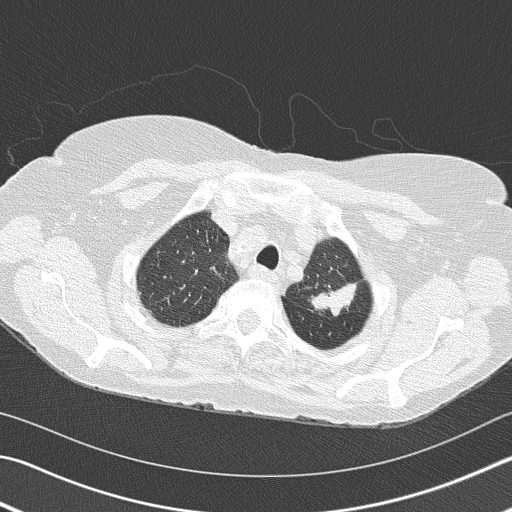
Chest CT (low-dose screening protocol), one axial image; second screening round (one year after baseline); lung window (W 1500 / L -600 HU); lung (sharp) reconstruction kernel (B50f); slice 133 of 153 in the series. Female participant, aged 68 years at enrolment.
Lesion marked by an expert reader, bounding box <289,243,370,328> (left, top, right, bottom; pixels). The exam's reader record, not a measurement of the box and not confirmed to be the same lesion: non-calcified nodule or mass ≥4 mm, left upper lobe, 4 × 2 mm, spiculated (stellate) margins, soft tissue attenuation, pre-existing on the prior screen: yes; interval growth: yes. Official screen result: positive, other. Later outcome: lung cancer diagnosed 392 days after this screen — adenocarcinoma, NOS, left upper lobe, poorly differentiated (G3), stage IB (AJCC 6th edition), 50 mm at pathology.